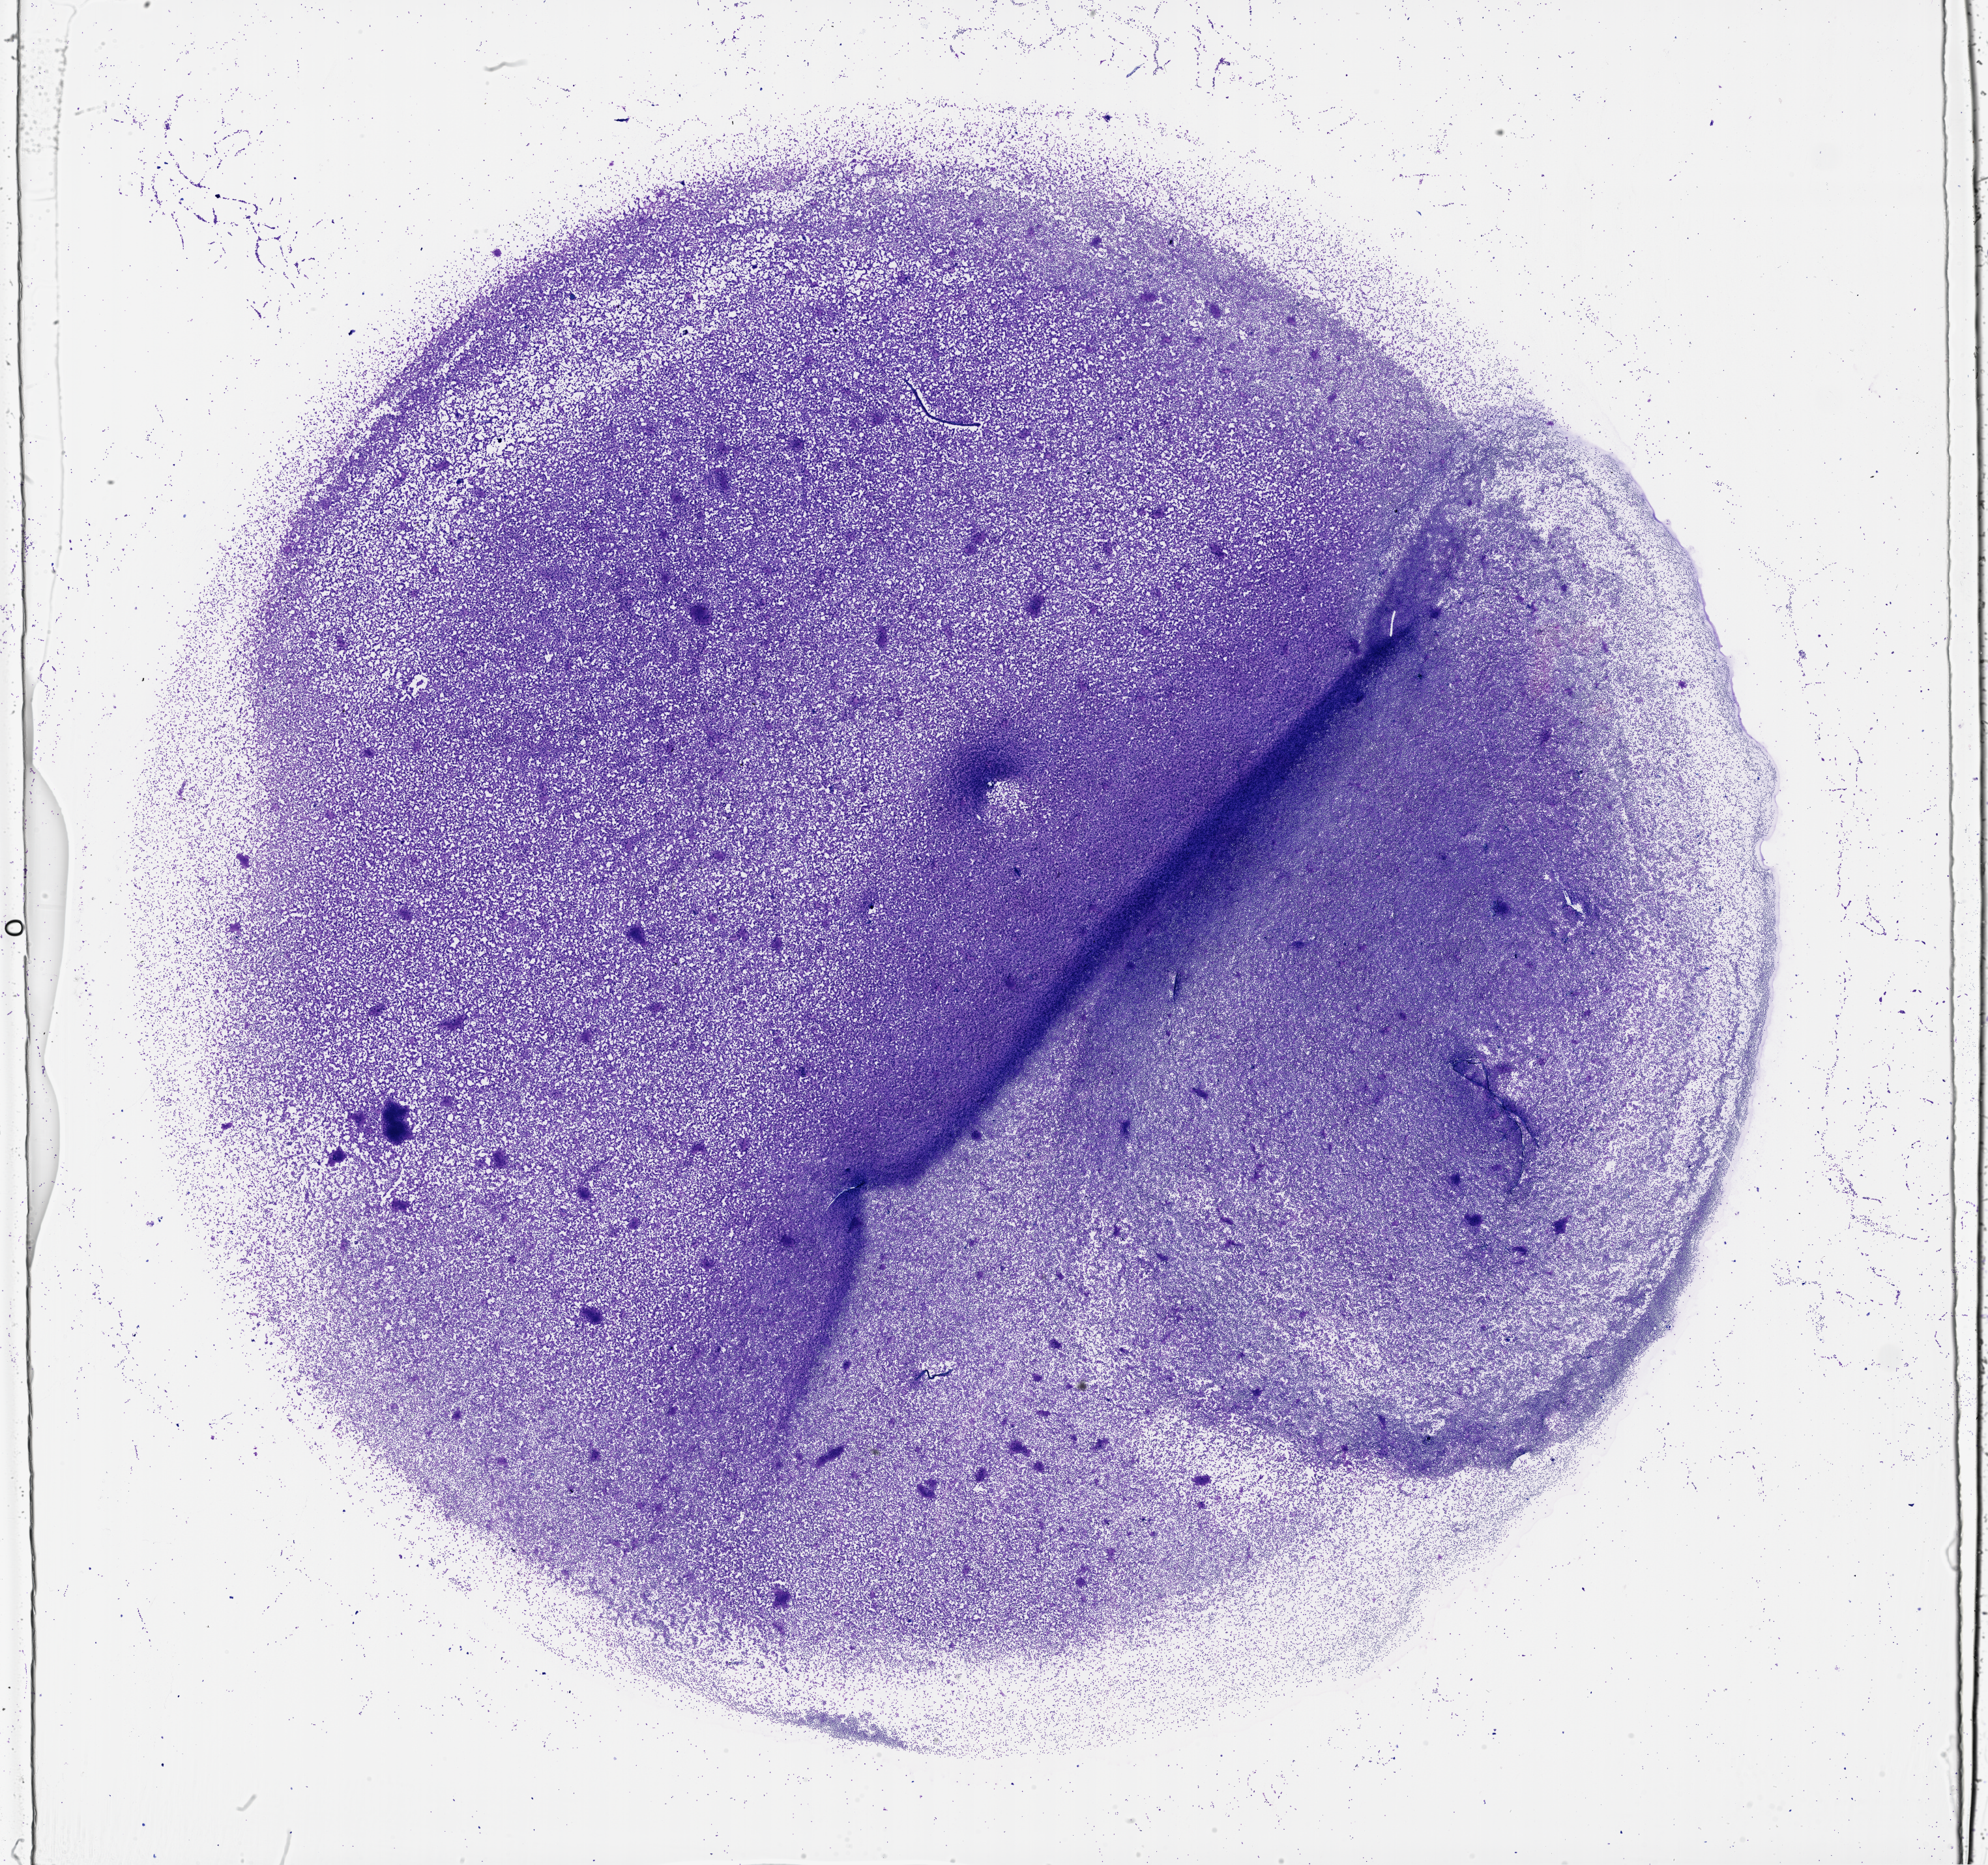
Whole-slide histology image, H&E, whole scanned area (about 24.6 x 23.1 mm, acquisition: 40x scan) shown as a low-resolution overview; bone marrow (leukaemic) sample. 69-year-old female patient. Blasts: 60%.
WHO classification: Acute monoblastic and monocytic leukemia. FAB classification: M5. Diagnosis: Acute Myeloid Leukemia.